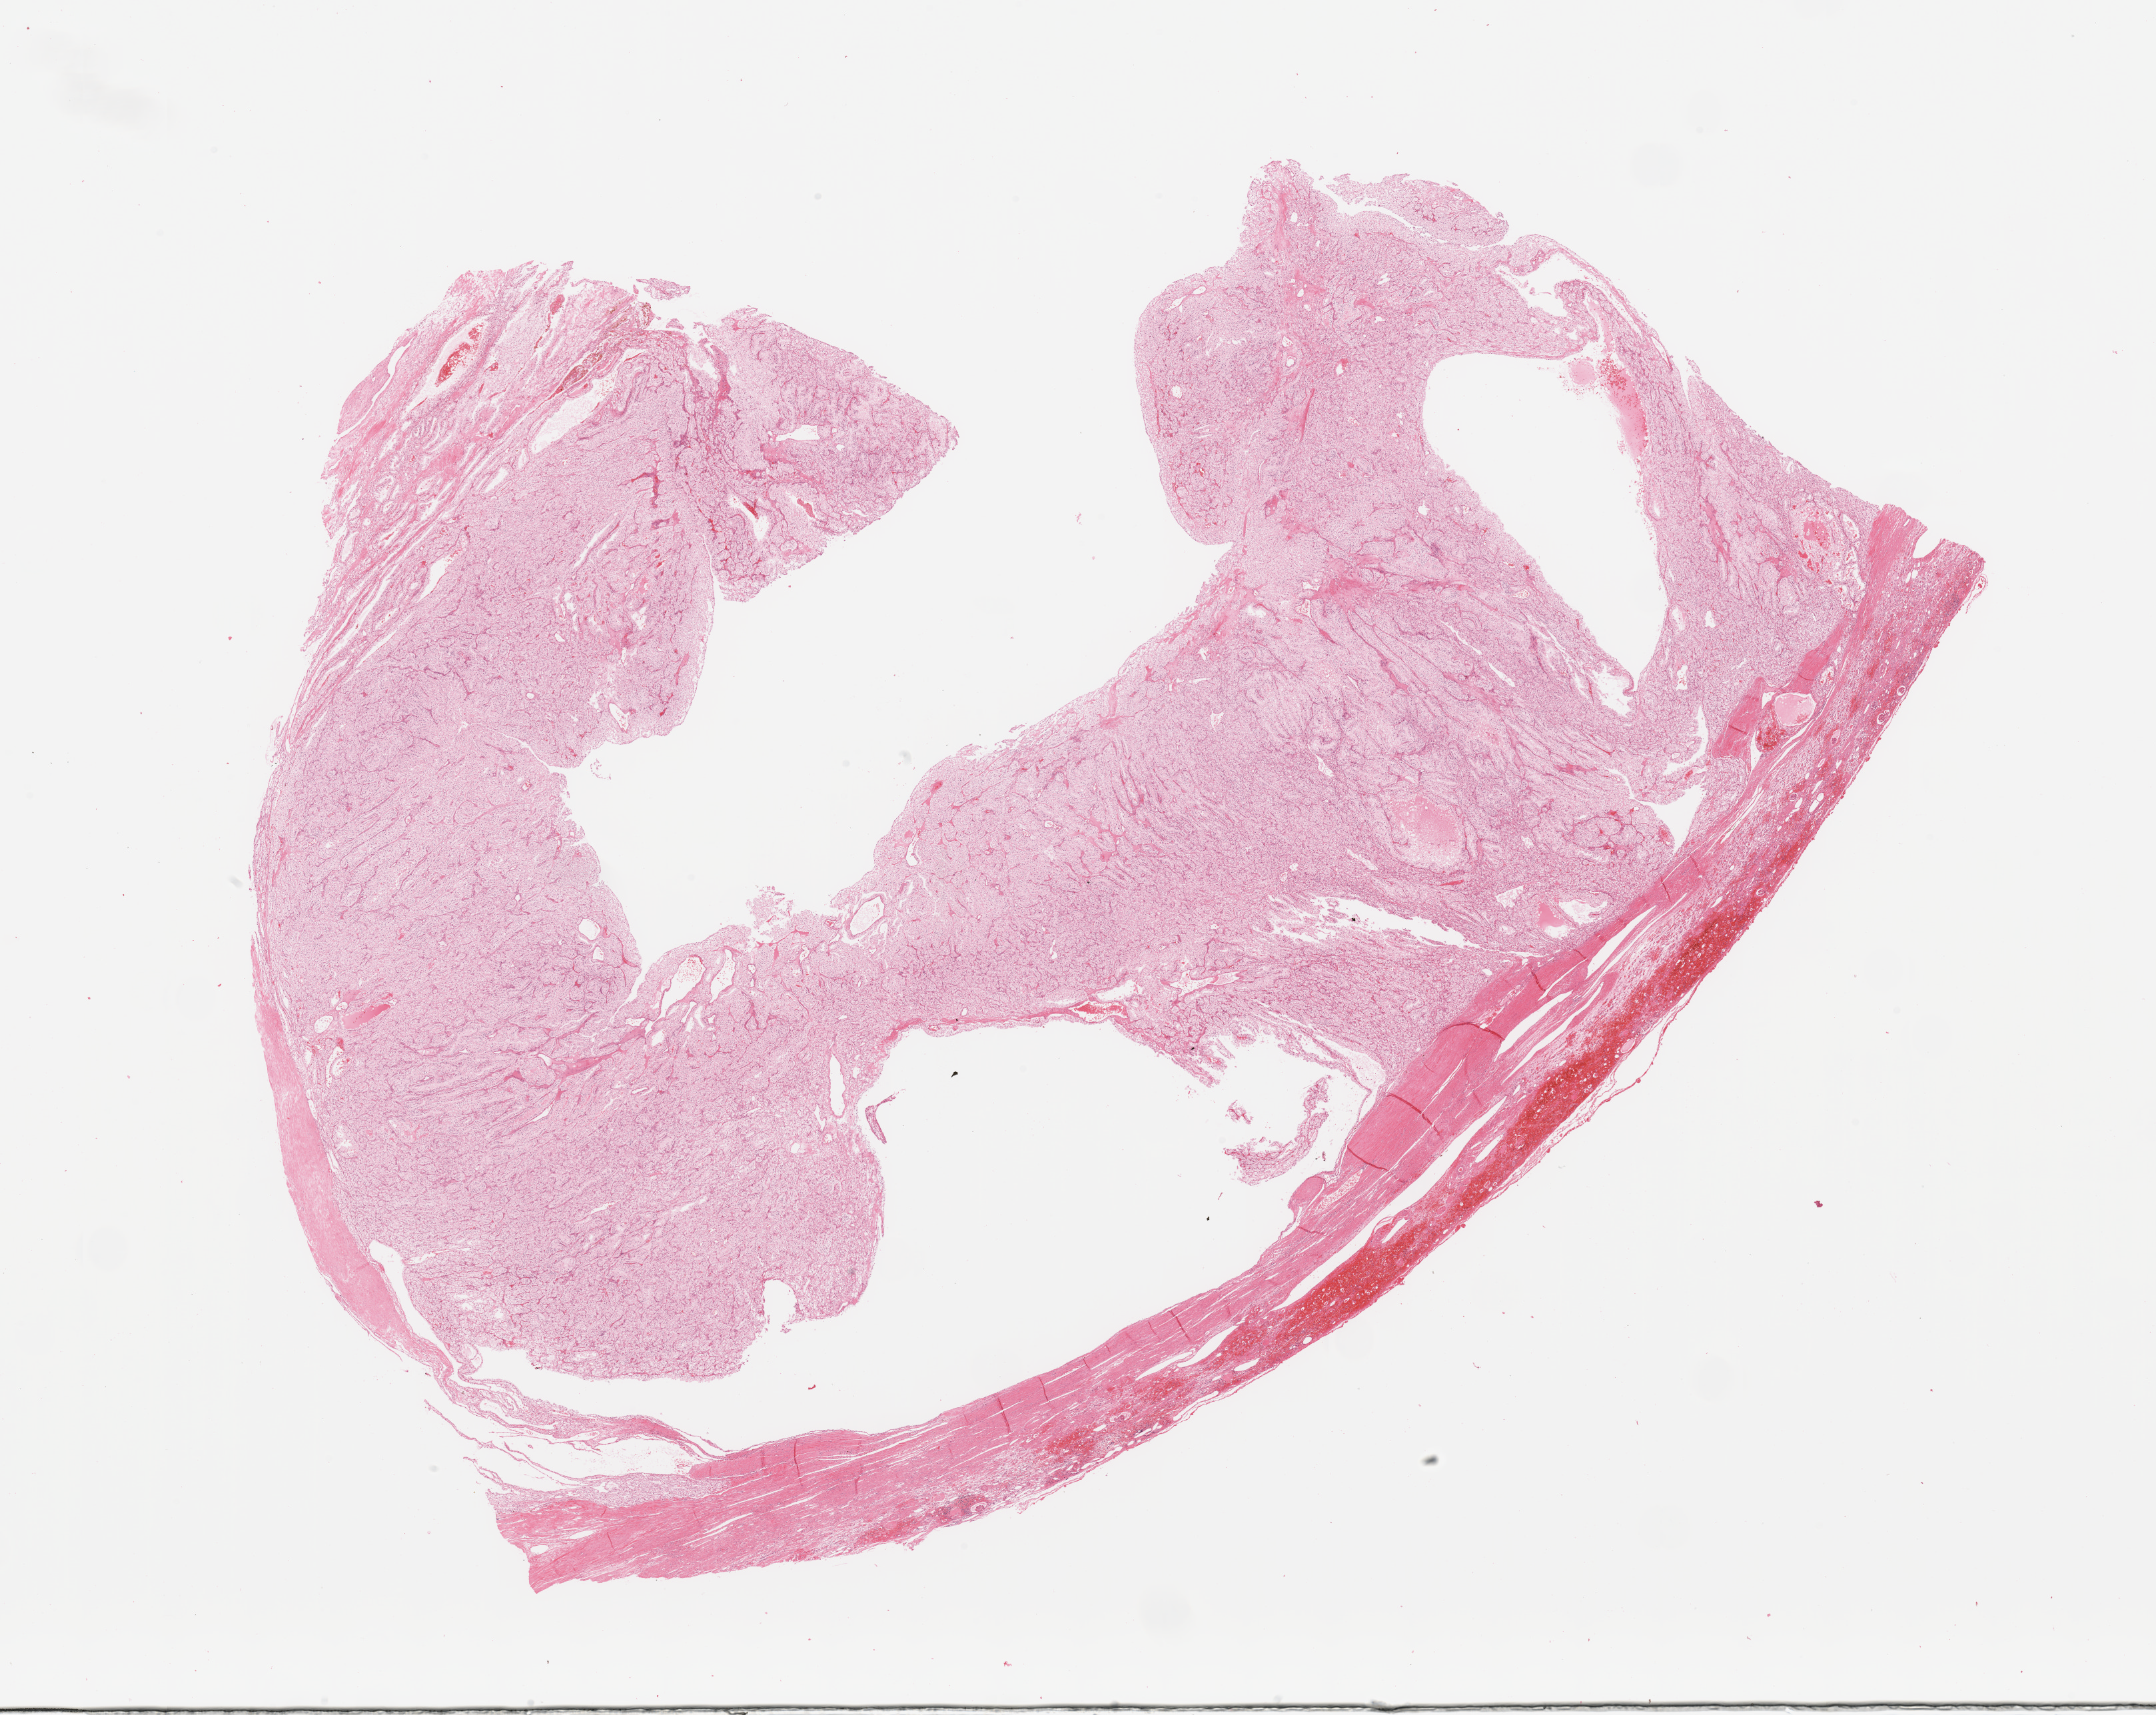
Whole-slide histology image, Hematoxylin and eosin (H&E) stained — whole scanned area (about 25.6 x 20.4 mm, acquisition: 20x scan) shown as a low-resolution overview; tumour tissue sample, kidney. Patient: male, age 51 years.
Diagnosis: Renal cell carcinoma, NOS.